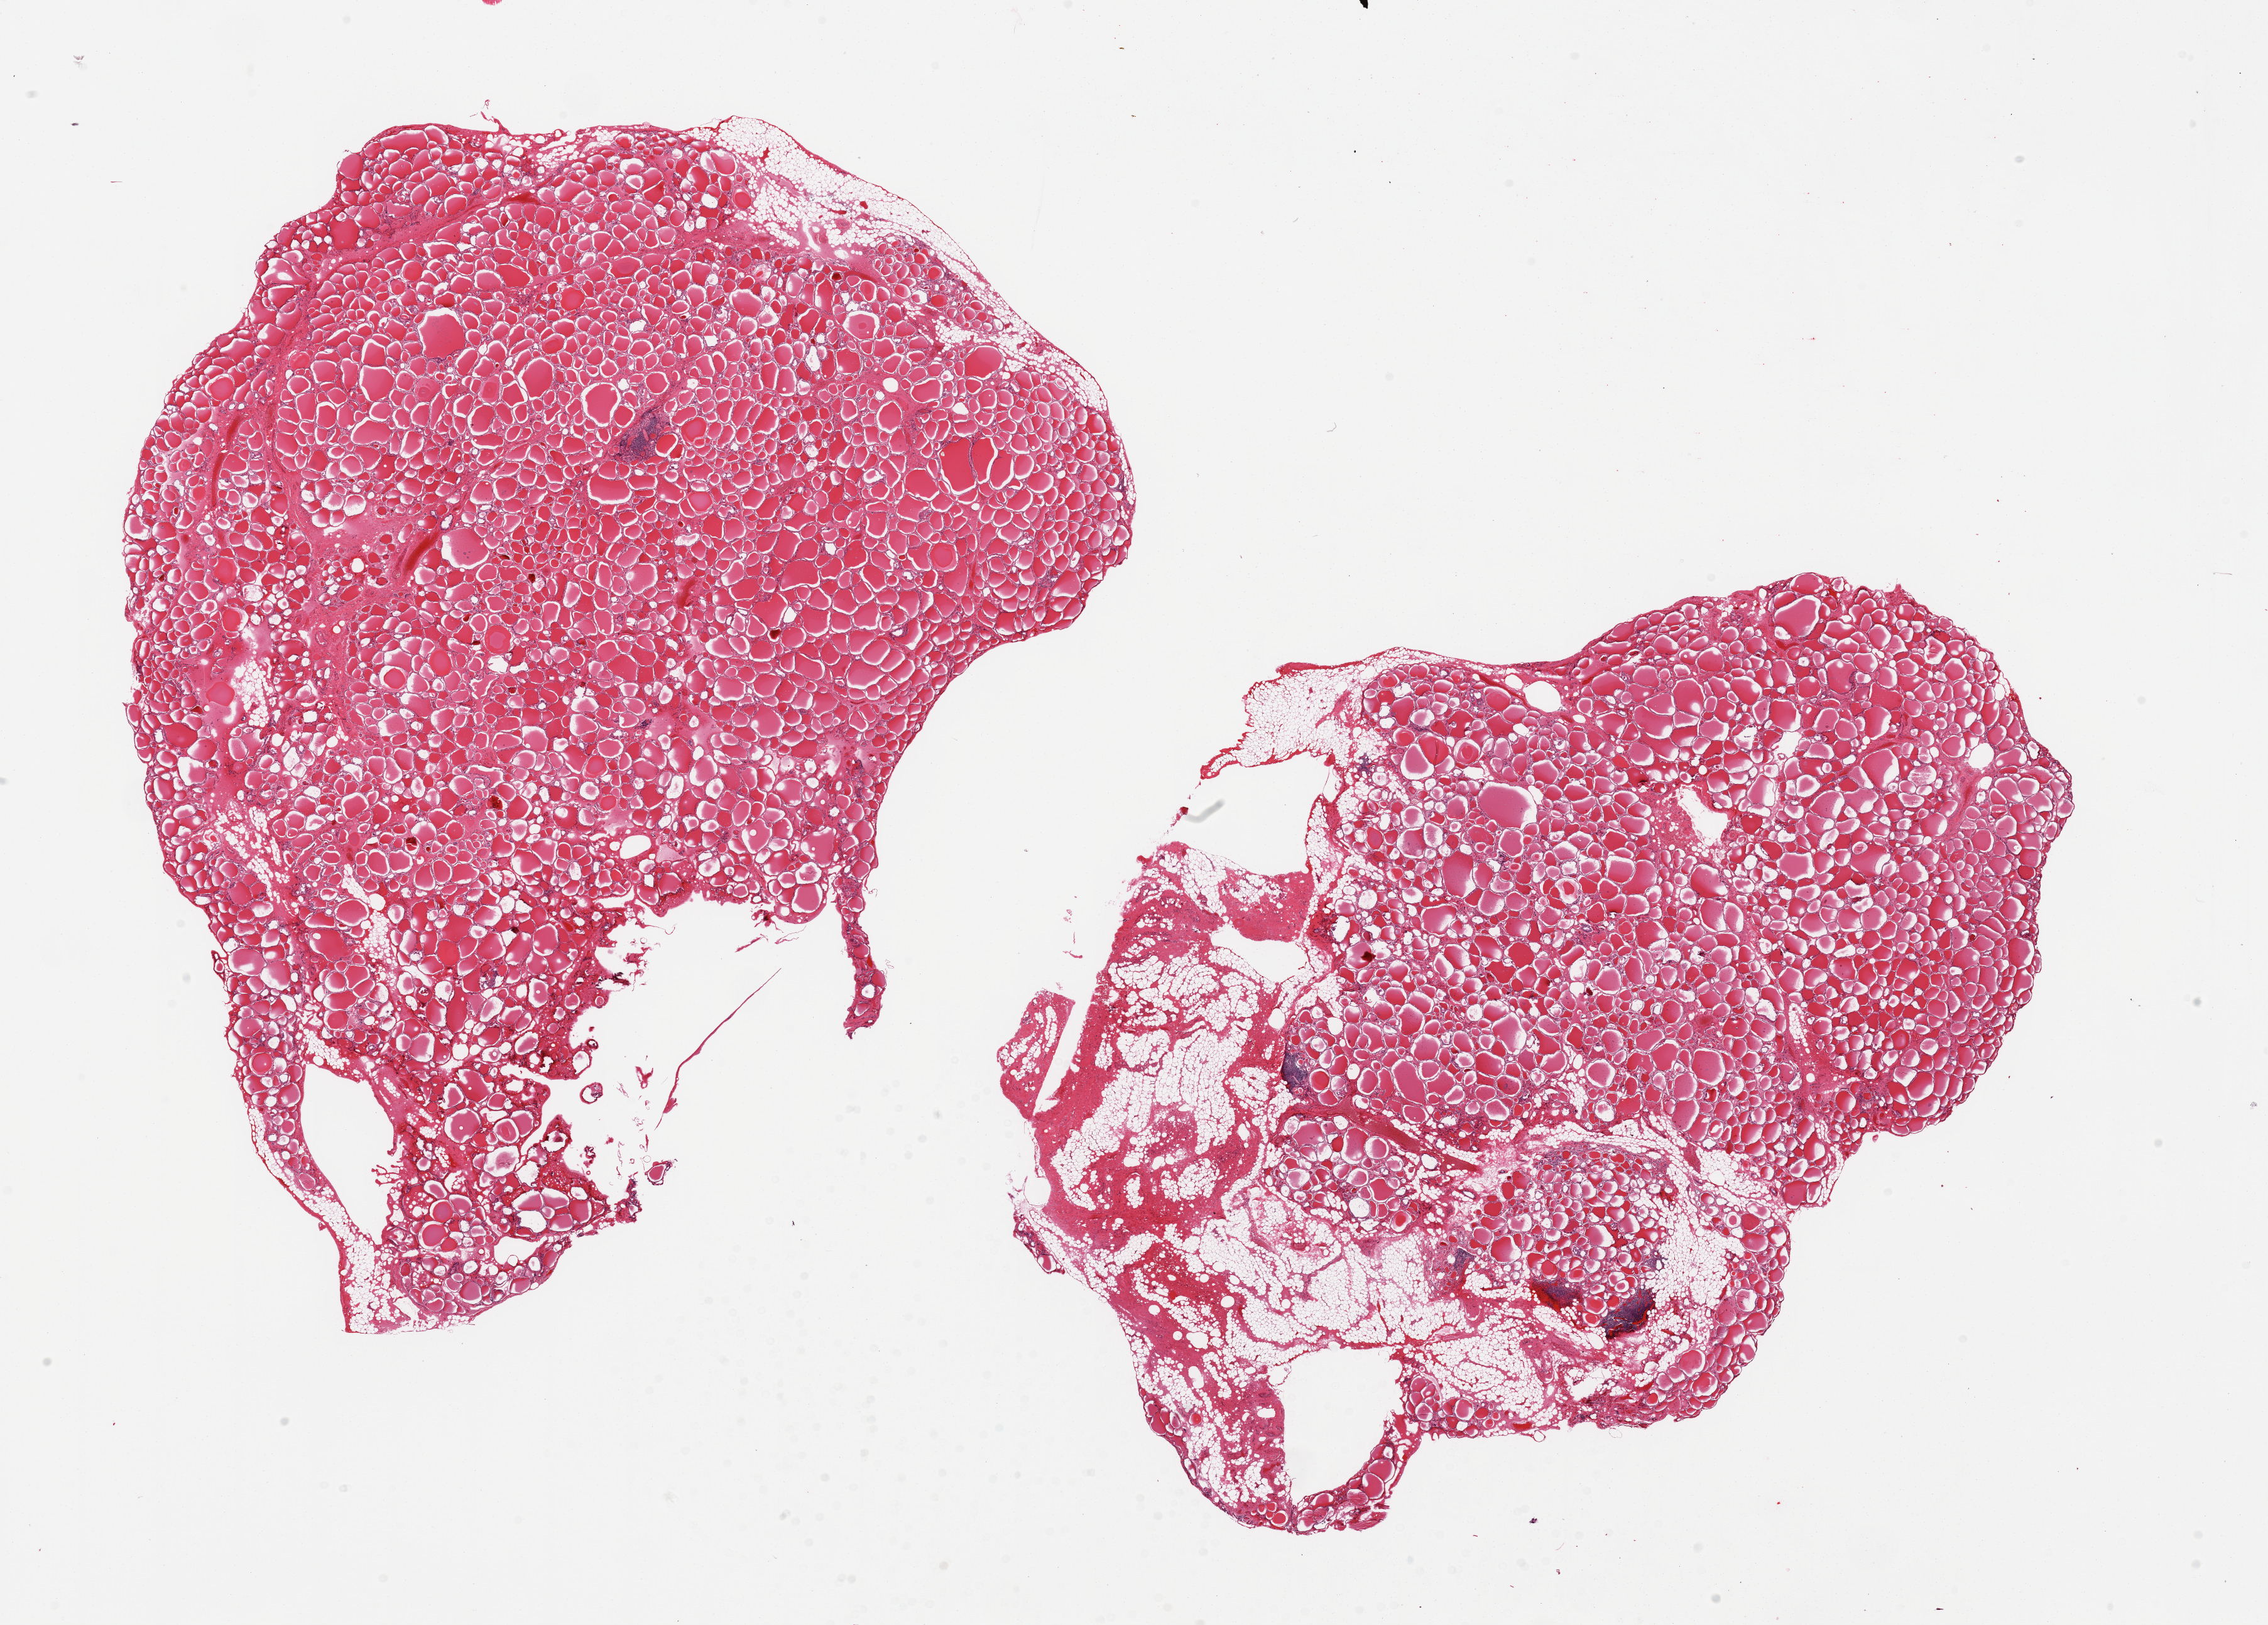
Digitized H&E-stained section — whole scanned area (about 28.5 x 20.5 mm) shown as a low-resolution overview, PAXgene-fixed, paraffin-embedded tissue, sampled site (target tissue): thyroid, donor tissue sample. Male donor.
Reviewer comment on this tissue sample: 2 pieces, one piece is ~30% fat/fibrous tissue, few collections of lymphocytes.